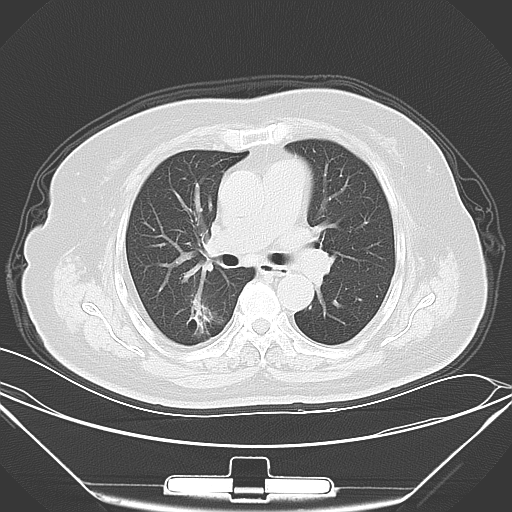
Chest CT, one axial slice. Slice 38 of 64 in the series (ordered by position). 120 kVp. Lung window (W 1500 / L -600 HU). 5 mm slice thickness. 512 × 512 image matrix. Female patient, age 70 years. Case-level facts recorded for this patient, not image findings: clinical TNM (as recorded): T2 N0 M3.
Structures marked on this image (bounding box drawn by a radiologist):
- lung tumour (recorded histology: adenocarcinoma): bounding box [x1, y1, x2, y2] px = [180, 297, 226, 337]